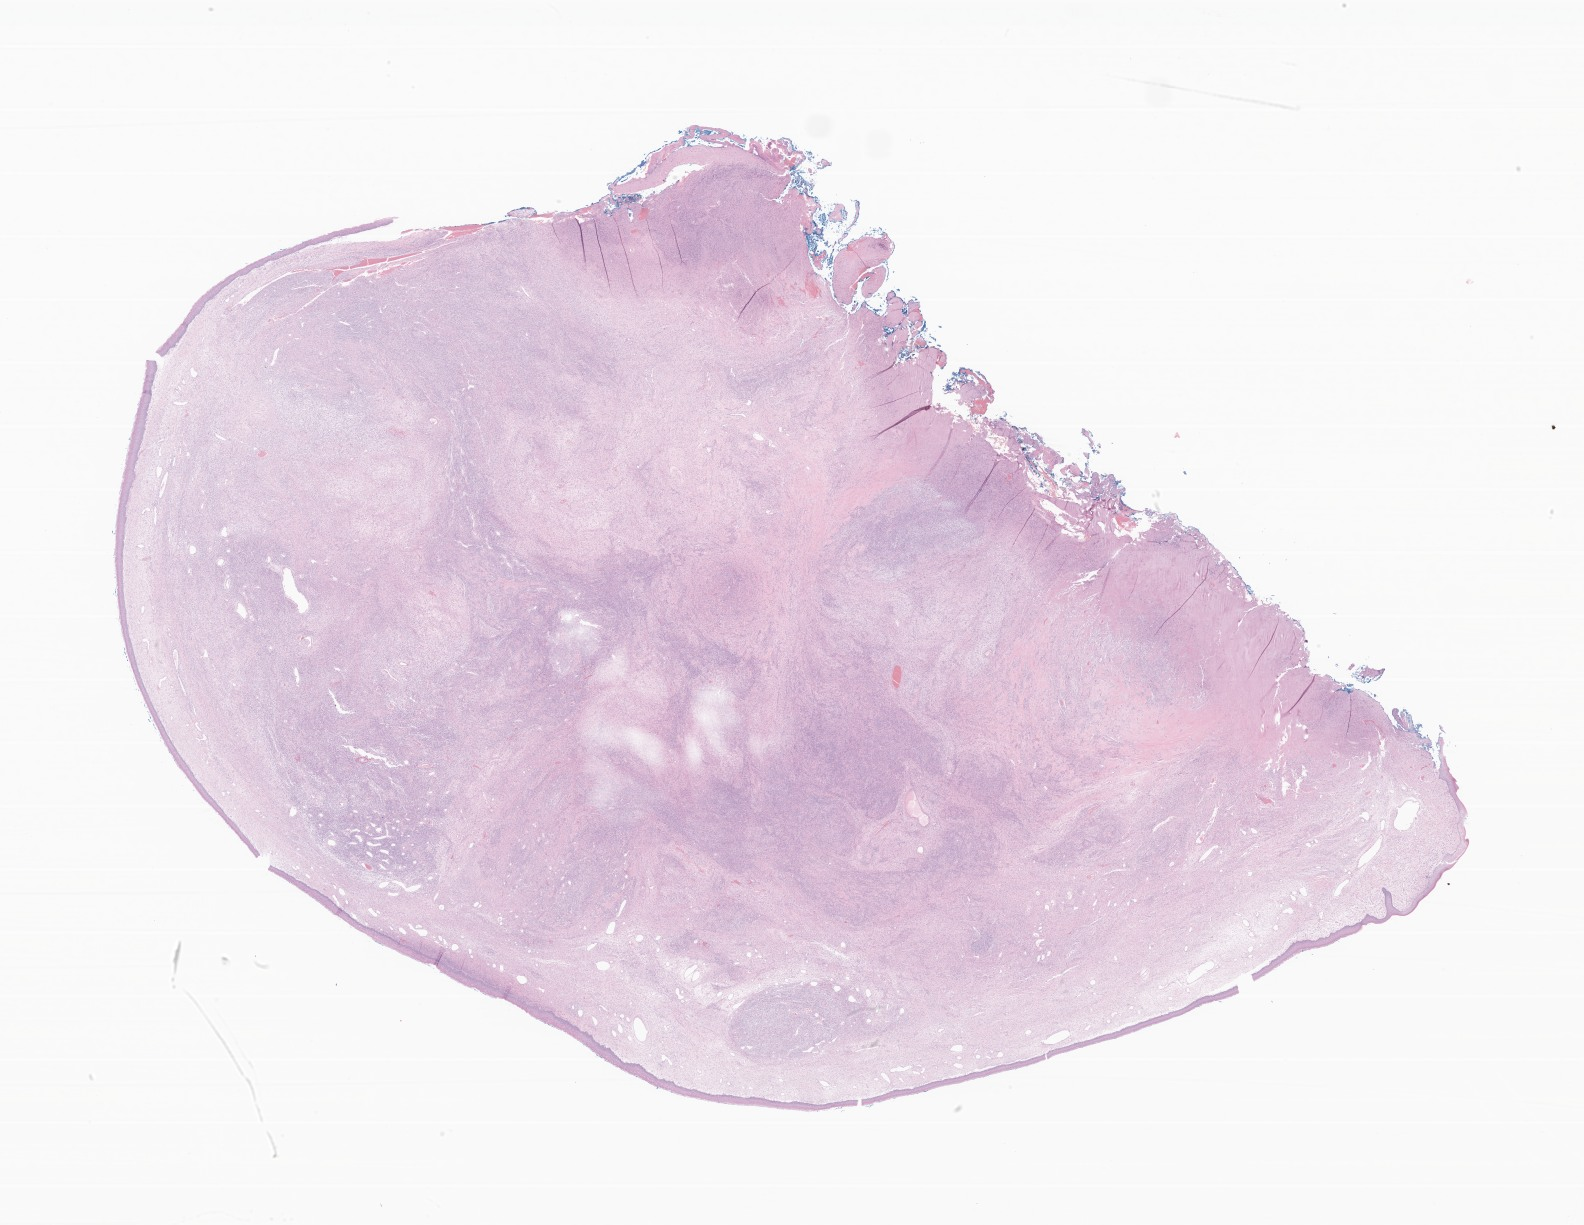
Digitized haematoxylin and eosin-stained section of tumor tissue from the head and neck, low-resolution overview of the scanned area, about 26.7 x 20.7 mm, formalin-fixed, paraffin-embedded (FFPE) tissue. Patient female; age 155 months (12 years 11 months).
* diagnosis (ICD-O-3 morphology term): Synovial sarcoma, NOS